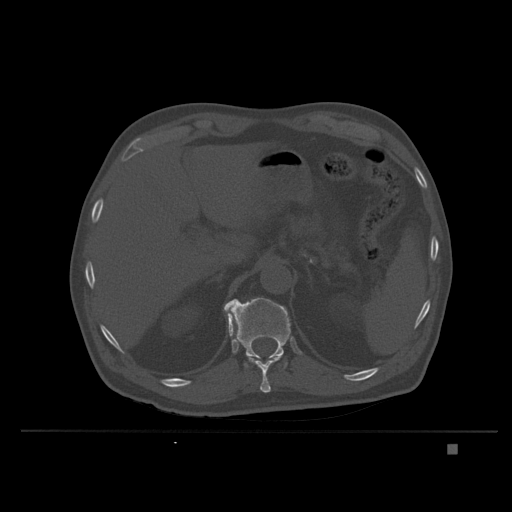
CT including the spine, one axial slice. Position 166 of 435 along the scan axis. Bone window (W 1800 / L 400 HU). 1.5 mm slice thickness. 512 × 512 image matrix. Male patient, age 73 years. From the clinical record (not read from this slice): primary cancer: skin.
Outlined on this slice (semi-automatically segmented with operator editing):
- T11 vertebra: bounding box <229,318,280,393> (left, top, right, bottom; pixels)
- T12 vertebra: <223,298,291,367>